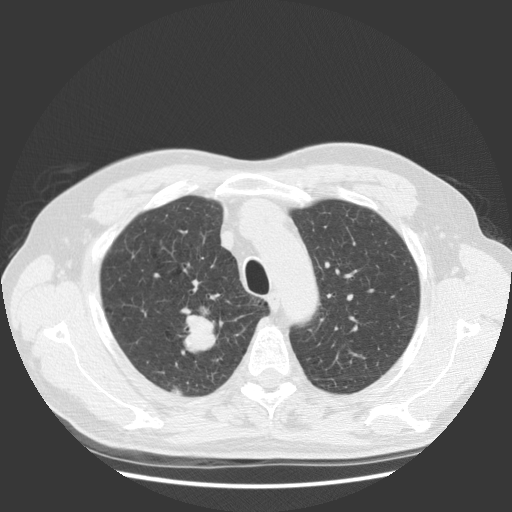
Chest CT (low-dose screening protocol), one axial image; baseline screening round; lung window (W 1500 / L -600 HU); 2.5 mm slice thickness; slice 99 of 131 in the series. Male participant, aged 63 years at enrolment.
- Expert reader's lesion annotation, bounding box [x1, y1, x2, y2] px = [158, 305, 230, 378].
- The screening reader recorded 2 non-calcified nodules or masses ≥4 mm on this exam; which of them this box marks is not recorded.
- Official screen result: positive, change unspecified: nodule(s) >= 4 mm or enlarging nodule(s), mass(es), or other non-specific abnormalities suspicious for lung cancer.
- Later outcome: lung cancer diagnosed 30 days after this screen — squamous cell carcinoma, NOS, right upper lobe, stage IIIB (AJCC 6th edition), 35 mm at pathology.